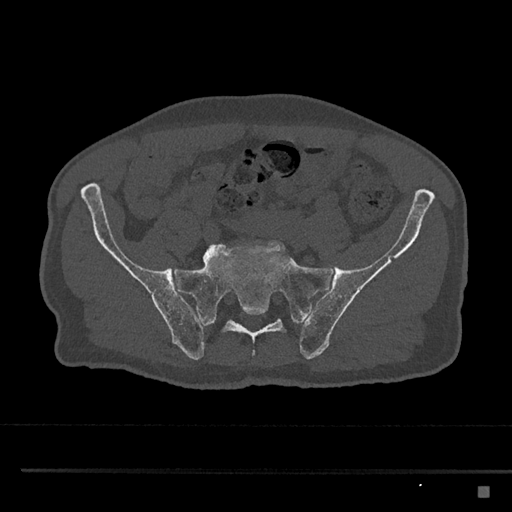
CT including the spine, one axial slice. Position 519 of 797 along the scan axis. Reconstruction kernel Br40s/3. Bone window (W 1800 / L 400 HU). 512 × 512 image matrix. Patient: male, 59 years. Case-level facts recorded for this patient, not image findings: primary cancer: prostate.
Outlined on this slice (semi-automatic segmentation, software-assisted and operator-edited):
- L5 vertebra: bounding box <203,253,210,261> (left, top, right, bottom; pixels)